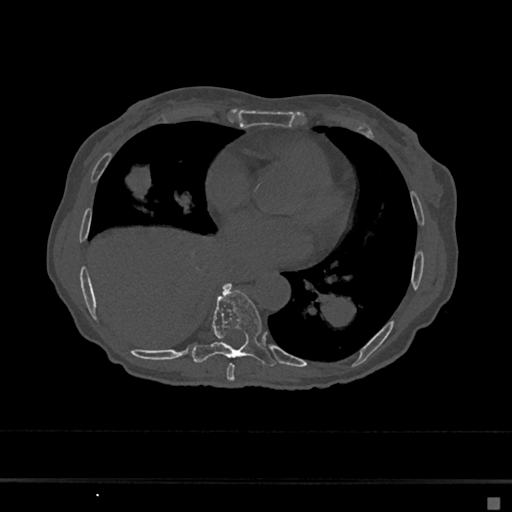
CT including the spine, one axial slice. Slice 329 of 797 in the series (ordered by position). Reconstruction kernel Br40s/3. 120 kVp. Bone window (W 1800 / L 400 HU). 512 × 512 image matrix, field of view 360 × 360 mm. Female patient, age 68 years. From the clinical record (not read from this slice): primary cancer: renal.
Structures marked on this image (semi-automatic segmentation, software-assisted and operator-edited):
- T7 vertebra: box from (x=227, y=363) to (x=235, y=381) px
- T8 vertebra: (x=192, y=283)–(x=275, y=367)